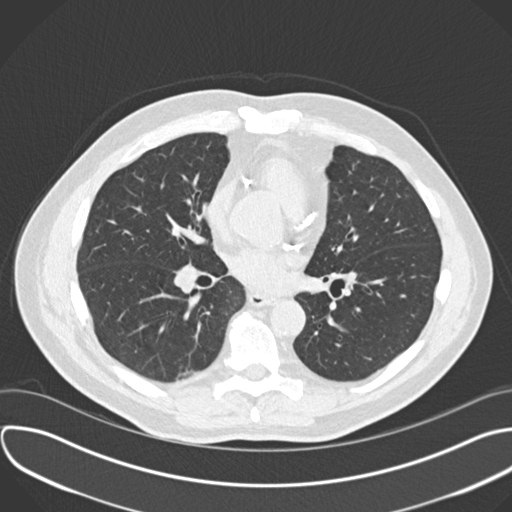
Low-dose screening chest CT, axial slice, baseline screening round, lung window (W 1500 / L -600 HU), 2 mm slice thickness, slice 98 of 205 in the series, 512 × 512 image matrix, field of view 384 × 384 mm. Male, age 68 years at enrolment. Former smoker at enrolment.
Expert-annotated lung lesion, bounding box <165,358,211,390> (left, top, right, bottom; pixels). Screening reader's record for this exam (one nodule recorded; not confirmed to be the boxed lesion): non-calcified nodule or mass ≥4 mm, lingula, 6 × 3 mm, smooth margins, soft tissue attenuation. Note: the box lies in the patient's right hemithorax on this image, whereas the reader's record names the left lung; they may be different findings. Official screen result: positive, change unspecified: nodule(s) >= 4 mm or enlarging nodule(s), mass(es), or other non-specific abnormalities suspicious for lung cancer. Lung cancer was diagnosed 817 days after this screen: adenosquamous carcinoma, right lower lobe, moderately differentiated (G2), stage IB (AJCC 6th edition), 31 mm at pathology.